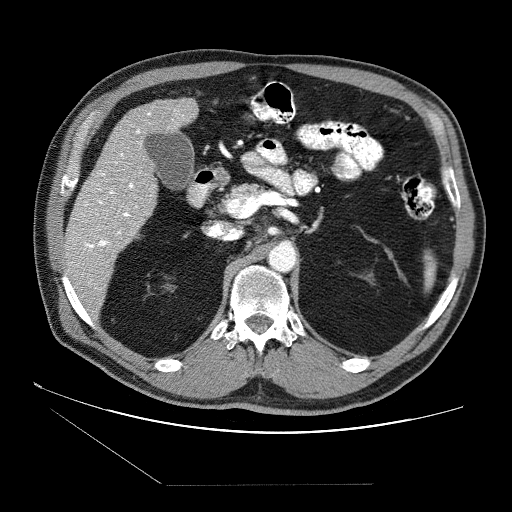
Contrast-enhanced abdominal CT (liver protocol), one axial slice. Position 34 of 87 along the scan axis. Reconstruction kernel STANDARD. Soft-tissue window (W 400 / L 40 HU). 2.5 mm slice thickness. 512 × 512 image matrix, field of view 400 × 400 mm. Case-level facts recorded for this patient, not image findings: diagnosis: hepatocellular carcinoma (patient treated with transarterial chemoembolisation; whether this scan precedes or follows treatment is not stated here); TNM stage (as recorded): Stage-II; Child-Pugh class: B; tumour differentiation: no biopsy; tumour nodularity: multinodular.
Annotated regions visible in this slice (semi-automatically segmented with operator editing):
- liver parenchyma outside the tumour (the mass and vessels are separate outlines, so this box may not span the whole liver): bounding box <64,98,198,308> (left, top, right, bottom; pixels)
- liver vessels: <81,113,151,250>